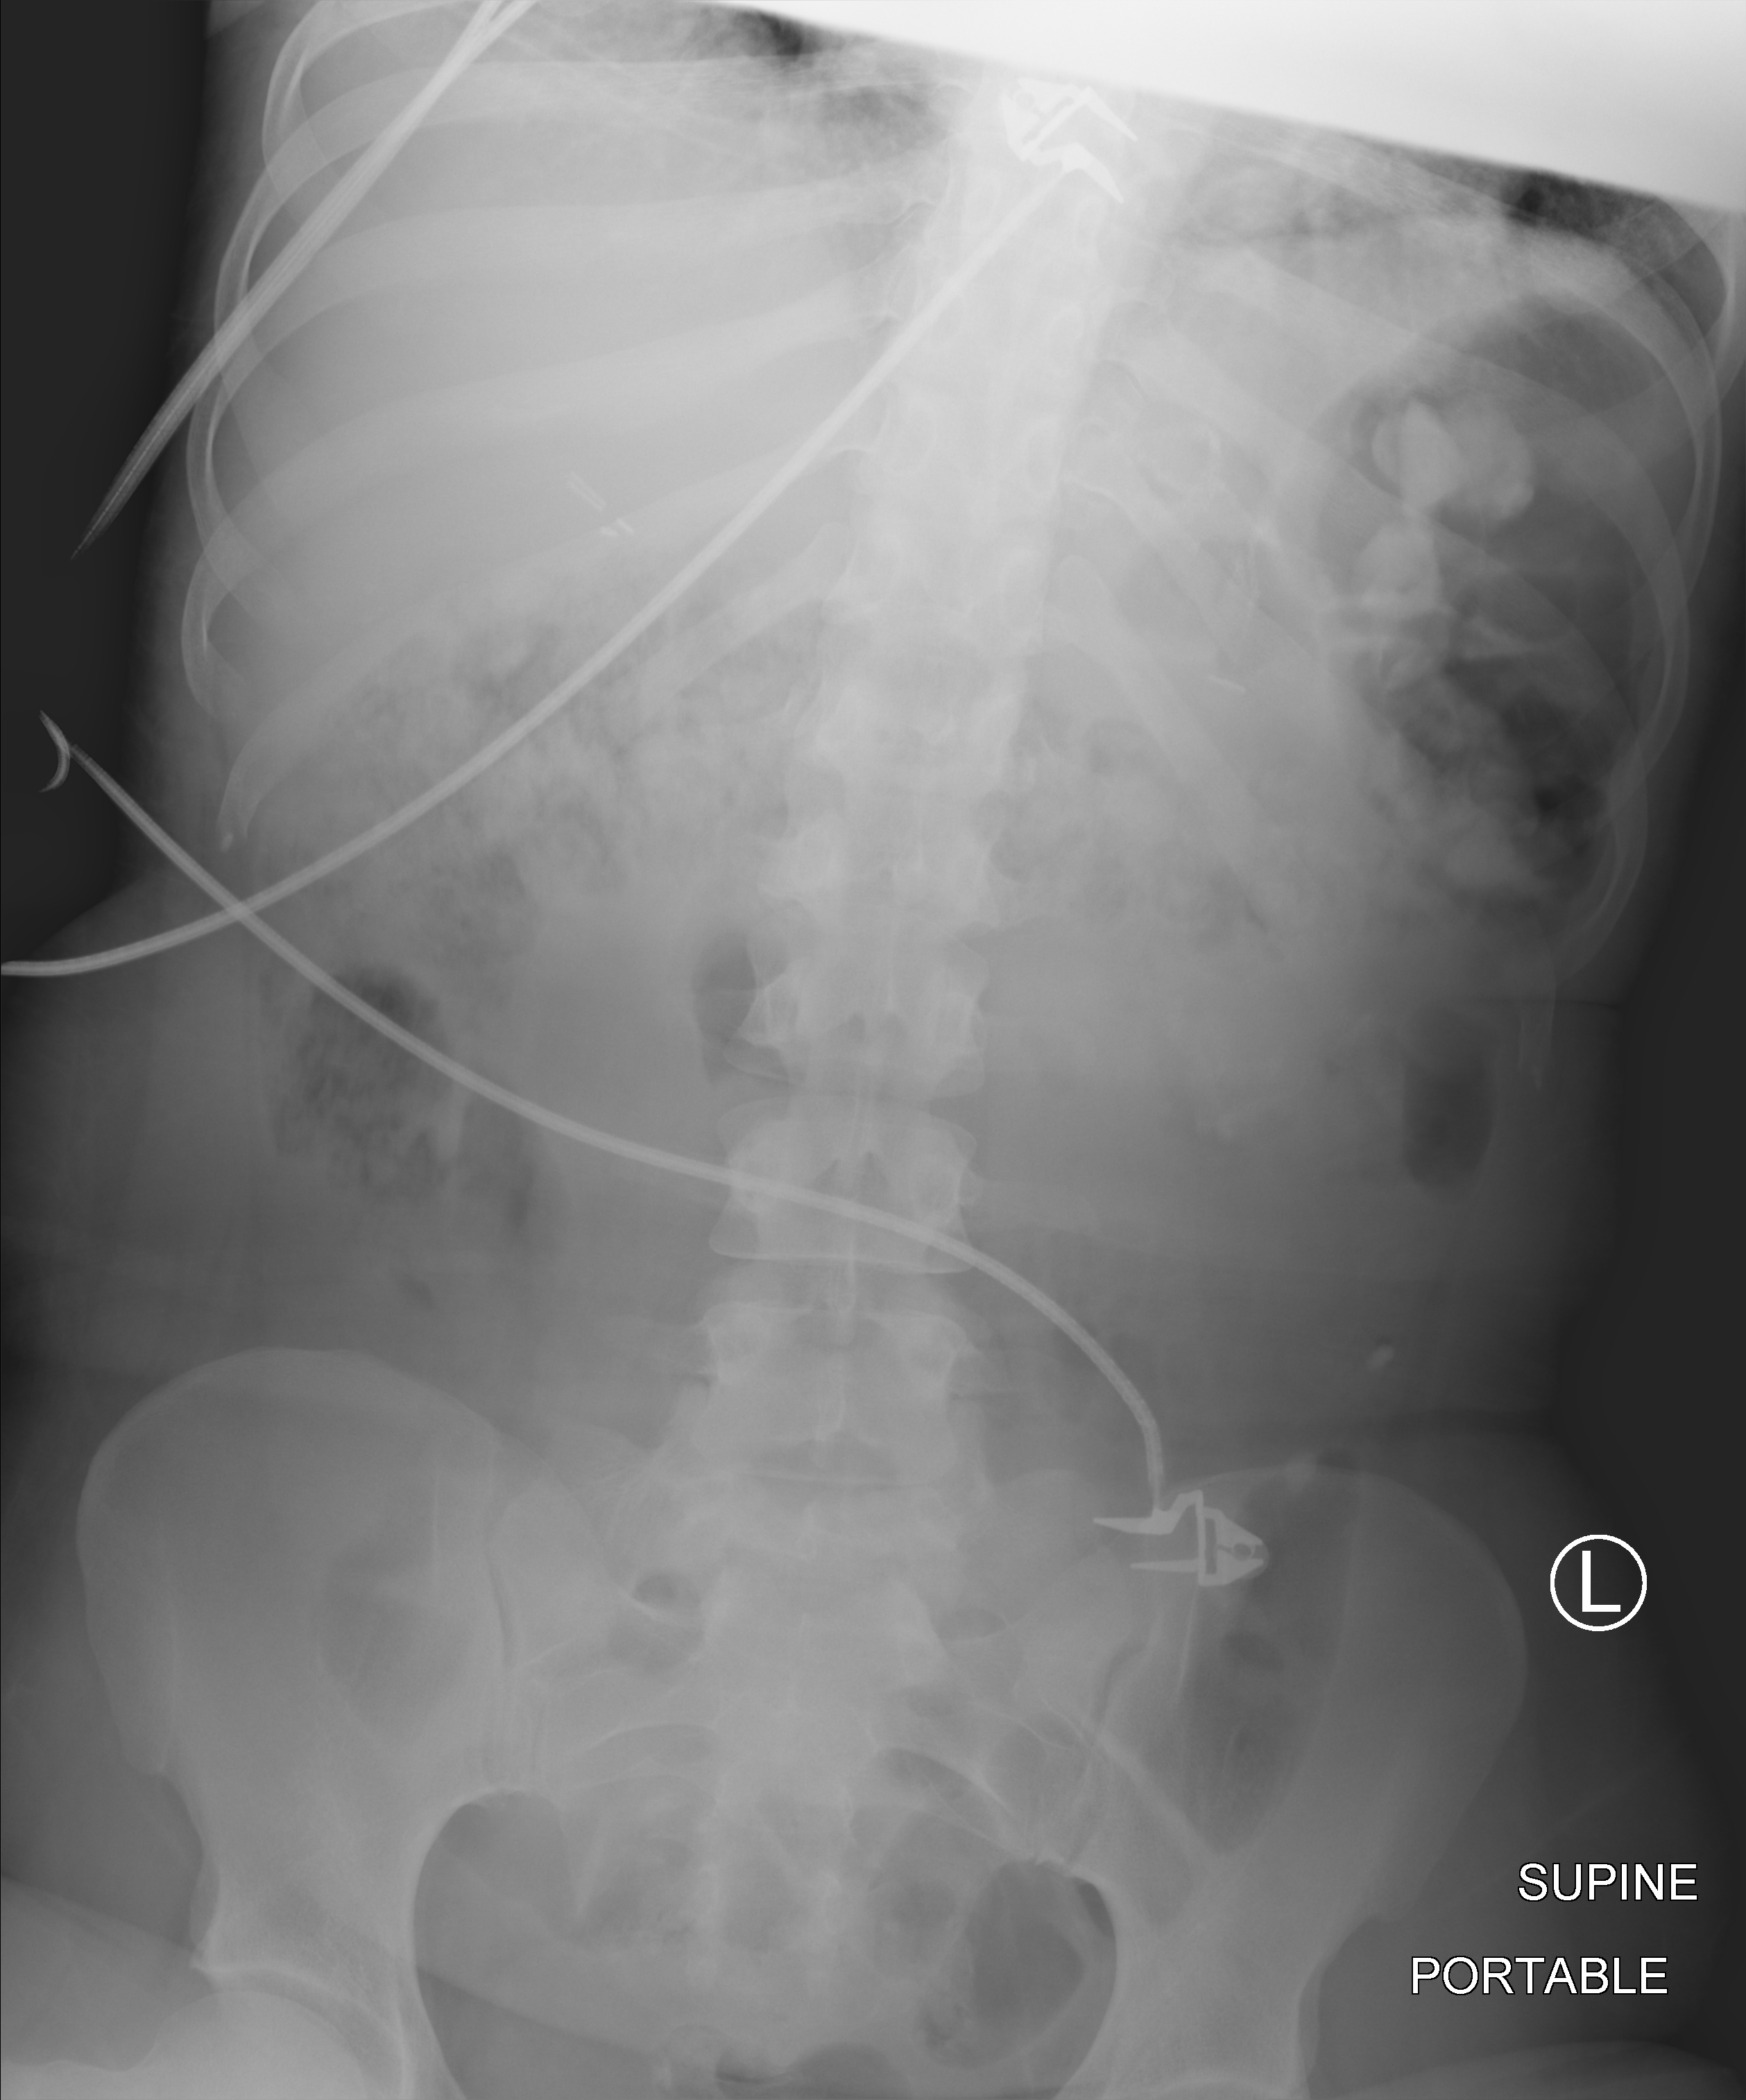
Abdomen X-ray (portable); anteroposterior (AP) projection. Patient hospitalised with COVID-19; female, aged 18–59 years.
From the hospital-stay record, not from the radiograph (when in the stay this image was taken is not recorded): mechanically ventilated during this hospital stay: no.